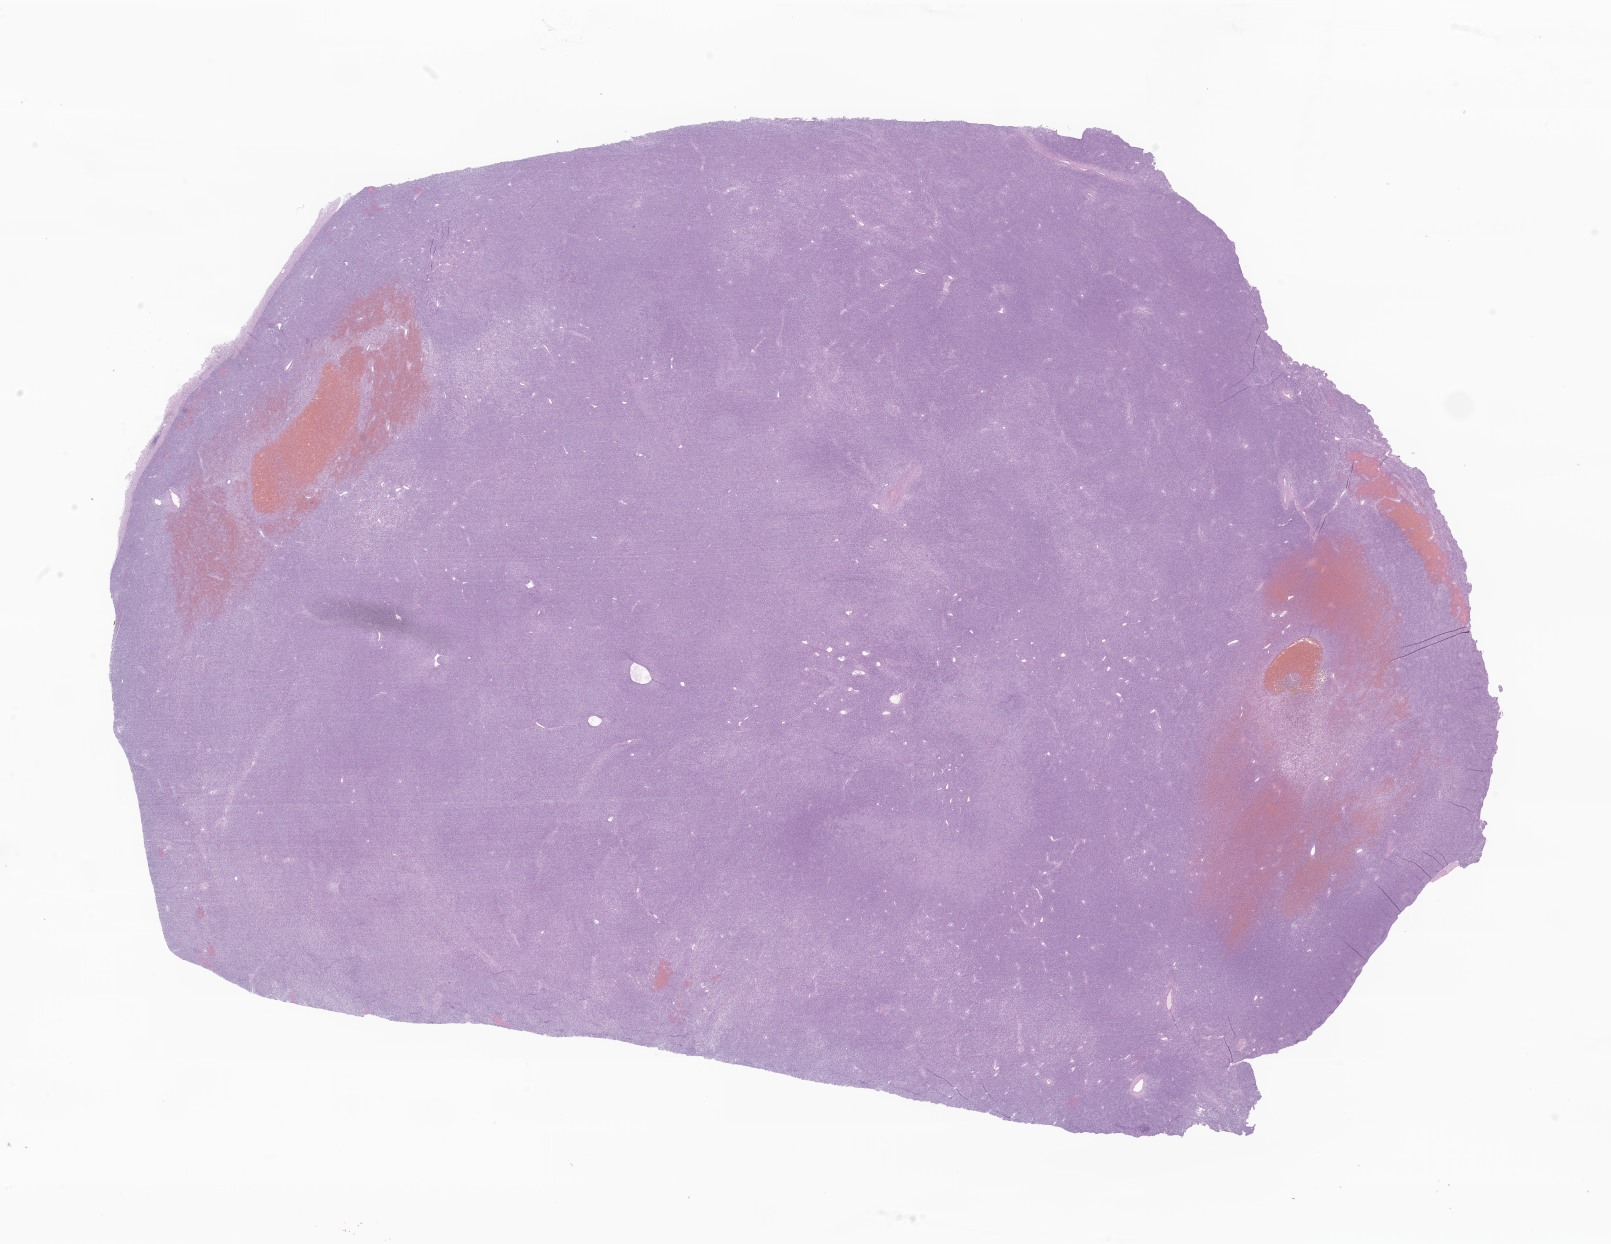
Whole-slide image, H&E stain of tumor tissue from the soft tissue of lower extremity, a low-resolution overview of the entire scanned area, about 27.2 x 21.0 mm, FFPE section. Male patient, age 188 months (15 years 8 months).
Recorded diagnosis: Synovial sarcoma, NOS.